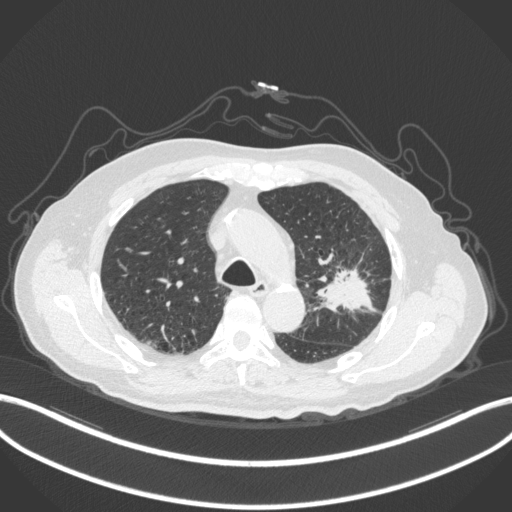
Chest CT, one axial slice. Slice 208 of 331 in the series (ordered by position). Lung window (W 1500 / L -600 HU). 1 mm slice thickness. 512 × 512 image matrix, field of view 400 × 400 mm. Patient: male, 79 years. Case-level facts recorded for this patient, not image findings: clinical TNM (as recorded): T2a N1 M1; histopathological grade: G3.
Outlined on this slice (rectangle marked by the reading radiologist):
- lung tumour (recorded histology: adenocarcinoma): bounding box <314,262,377,319> (left, top, right, bottom; pixels)